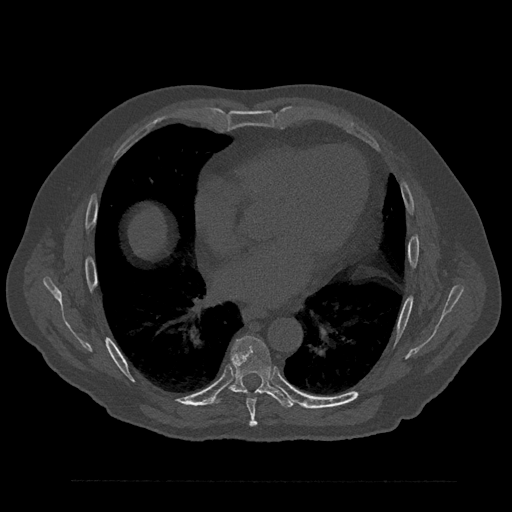
CT including the spine, one axial slice; position 476 of 797 along the scan axis; 120 kVp; bone window (W 1800 / L 400 HU); 0.5 mm slice thickness; 512 × 512 image matrix, field of view 430 × 430 mm. Patient: male, 61 years. From the clinical record (not read from this slice): primary cancer: prostate.
Annotated regions visible in this slice (semi-automatically segmented with operator editing):
- T7 vertebra: bounding box <241,390,259,426> (left, top, right, bottom; pixels)
- T8 vertebra: <214,335,295,408>